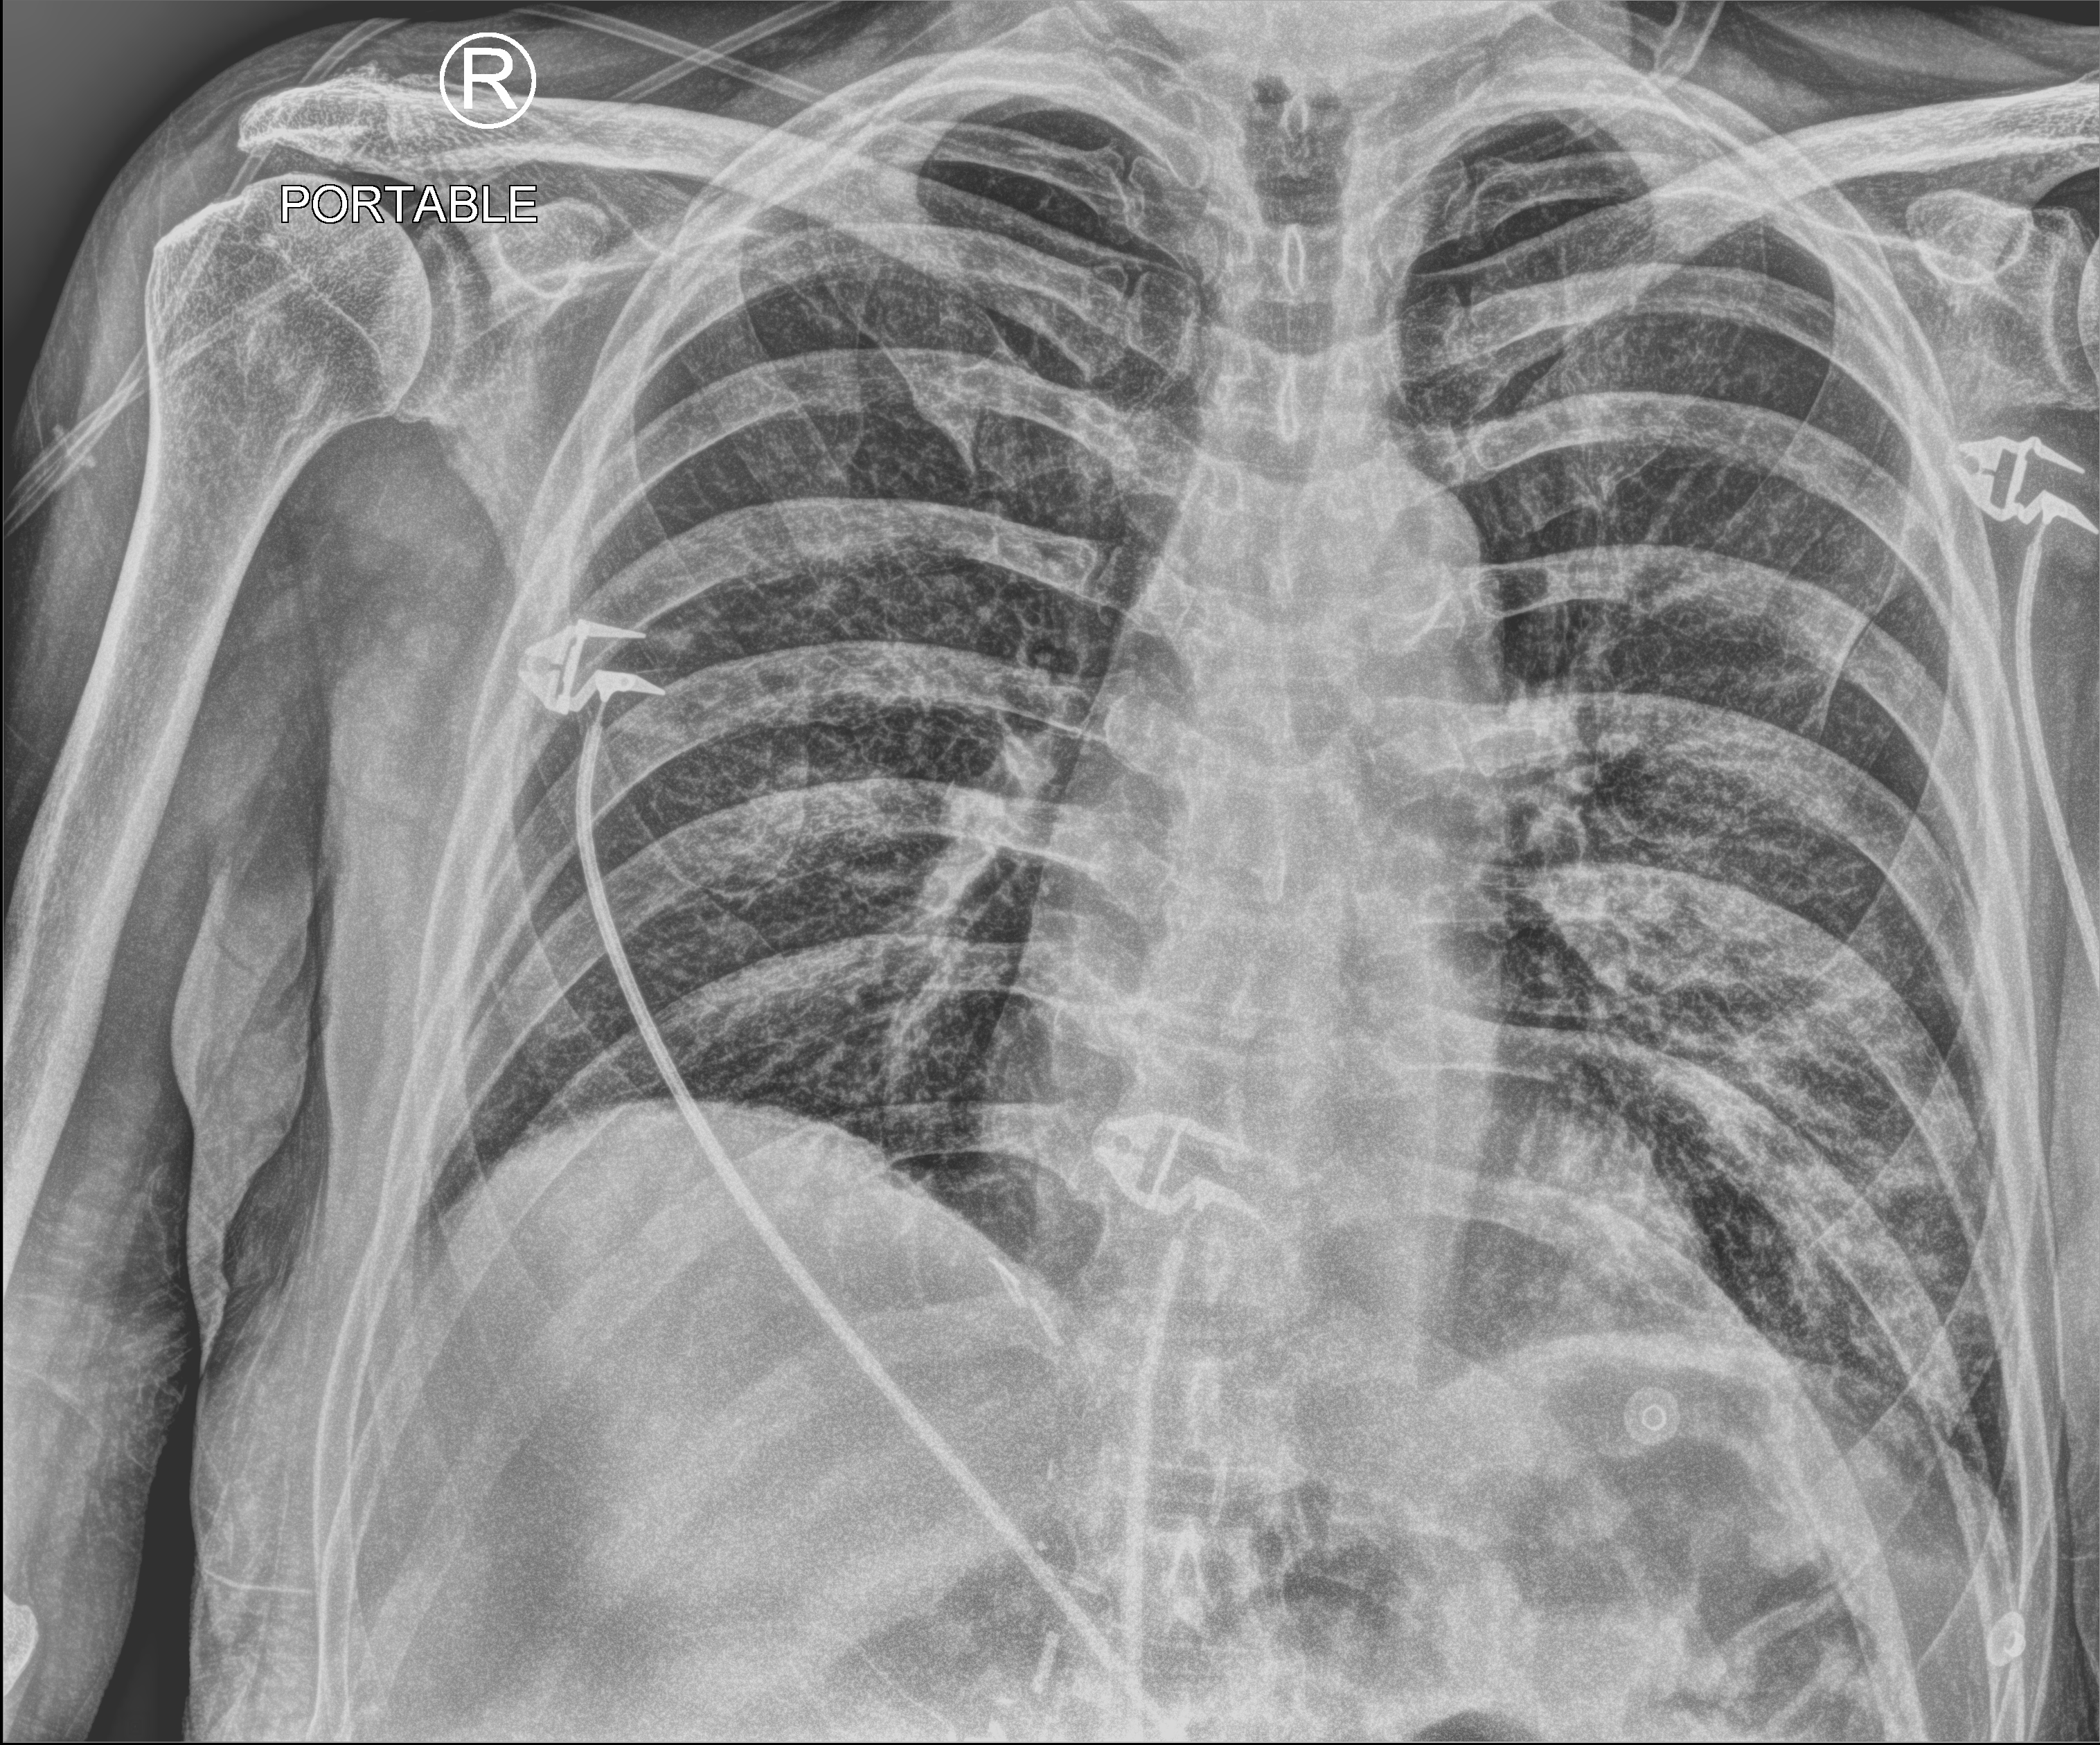
Portable chest radiograph, anteroposterior (AP) projection. Male patient hospitalised with COVID-19, age 60–74 years.
From the hospital-stay record, not from the radiograph (when in the stay this image was taken is not recorded): admitted to intensive care during this hospital stay: no.